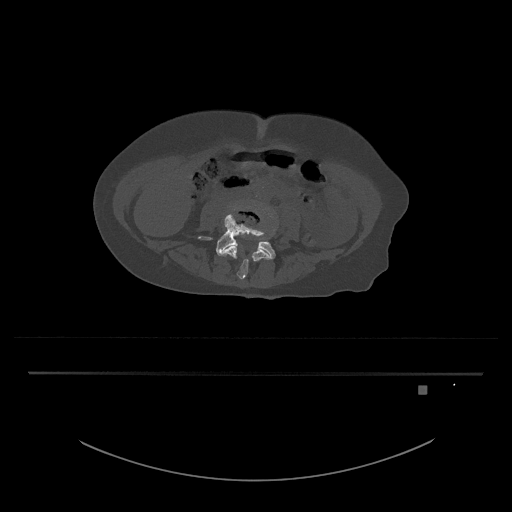
CT including the spine, one axial slice. 120 kVp. Bone window (W 1800 / L 400 HU). 0.5 mm slice thickness. 512 × 512 image matrix, field of view 500 × 500 mm. Patient: female, 57 years. From the clinical record (not read from this slice): primary cancer: cervical.
Outlined on this slice (semi-automatically segmented with operator editing):
- L4 vertebra: bounding box [x1, y1, x2, y2] px = [221, 206, 273, 280]